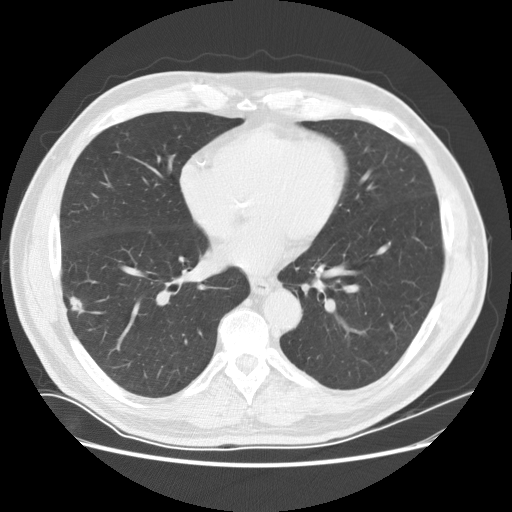
Low-dose screening chest CT, one axial slice. Position 75 of 169 along the scan axis. 120 kVp. Lung window (W 1500 / L -600 HU). 2.5 mm slice thickness. 512 × 512 image matrix.
Outlined on this slice (manually delineated by an expert):
- lesion 1 (tumor, lower lobe of right lung): bounding box [x1, y1, x2, y2] px = [70, 296, 85, 314]